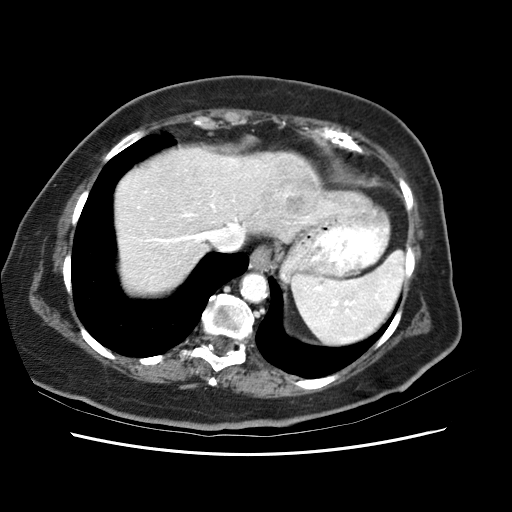
Contrast-enhanced abdominal CT (liver protocol), one axial slice. Slice 53 of 62 in the series (ordered by position). 120 kVp. Soft-tissue window (W 400 / L 40 HU). 2.5 mm slice thickness. 512 × 512 image matrix, field of view 340 × 340 mm. From the clinical record (not read from this slice): diagnosis: hepatocellular carcinoma (patient treated with transarterial chemoembolisation; whether this scan precedes or follows treatment is not stated here); TNM stage (as recorded): Stage-I; Child-Pugh class: B; tumour size: 5.3 cm.
Structures marked on this image (semi-automatic segmentation, software-assisted and operator-edited):
- abdominal aorta: bounding box (x1, y1, x2, y2) in pixels: (242, 274, 266, 302)
- liver parenchyma outside the tumour (the mass and vessels are separate outlines, so this box may not span the whole liver): (120, 148, 350, 276)
- mass: (269, 157, 316, 209)
- liver vessels: (153, 175, 312, 222)